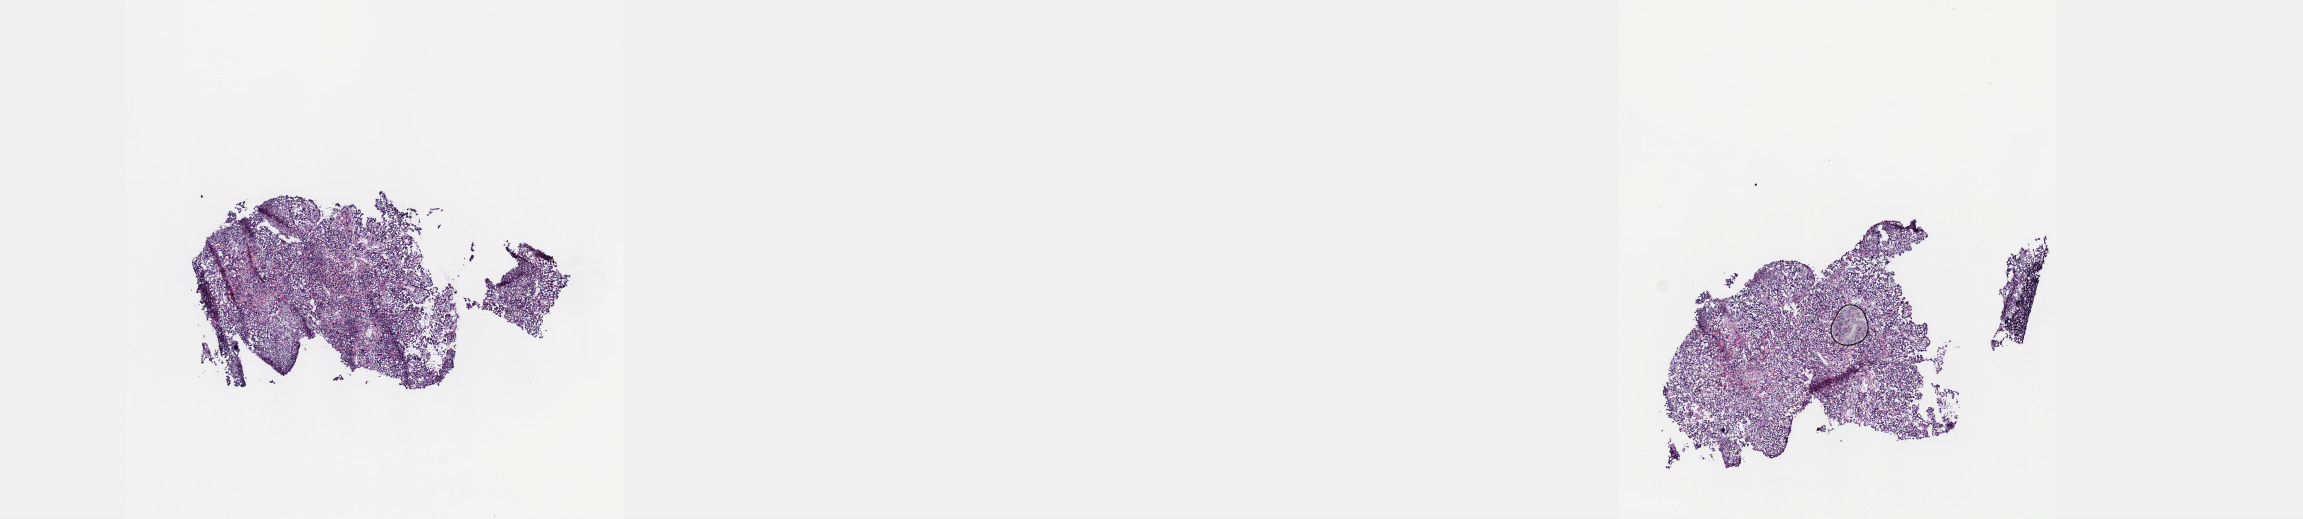
Whole-slide histology image, H&E-stained, shown as a low-resolution overview of the whole scanned area (about 18.6 x 4.2 mm, from a 40x scan), frozen section from the top of the tissue portion, mesothelium, primary tumour sample. Patient: male, age at initial diagnosis 73 years. Slide review estimates, as recorded: tumour cells 80%, tumour nuclei 80%.
Diagnosis: Mesothelioma, biphasic, malignant (pleura, NOS).